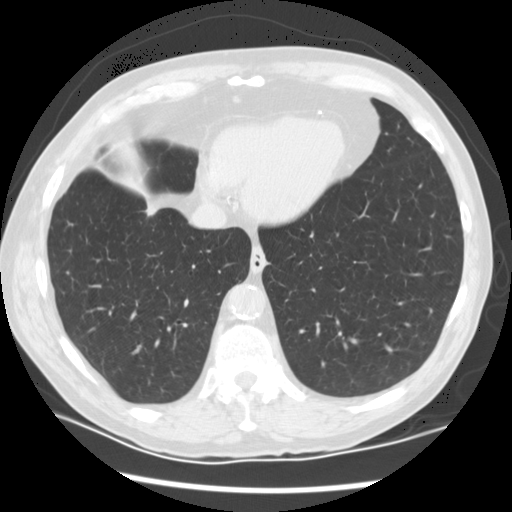
Chest CT (low-dose screening protocol), one axial image, baseline annual screen, lung window (W 1500 / L -600 HU), 2.5 mm slice thickness, slice 95 of 122 in the series. Male, age 68 years at enrolment.
• Expert reader's lesion annotation, bounding box [x1, y1, x2, y2] px = [119, 192, 175, 236].
• The screening reader recorded 3 non-calcified nodules or masses ≥4 mm on this exam (right upper lobe, right upper lobe, right lower lobe); which of them this box marks is not recorded.
• Later outcome: lung cancer diagnosed 90 days after this screen — adenocarcinoma, NOS, right upper lobe, right lower lobe, well differentiated (G1), stage IV (AJCC 6th edition), 35 mm at pathology.